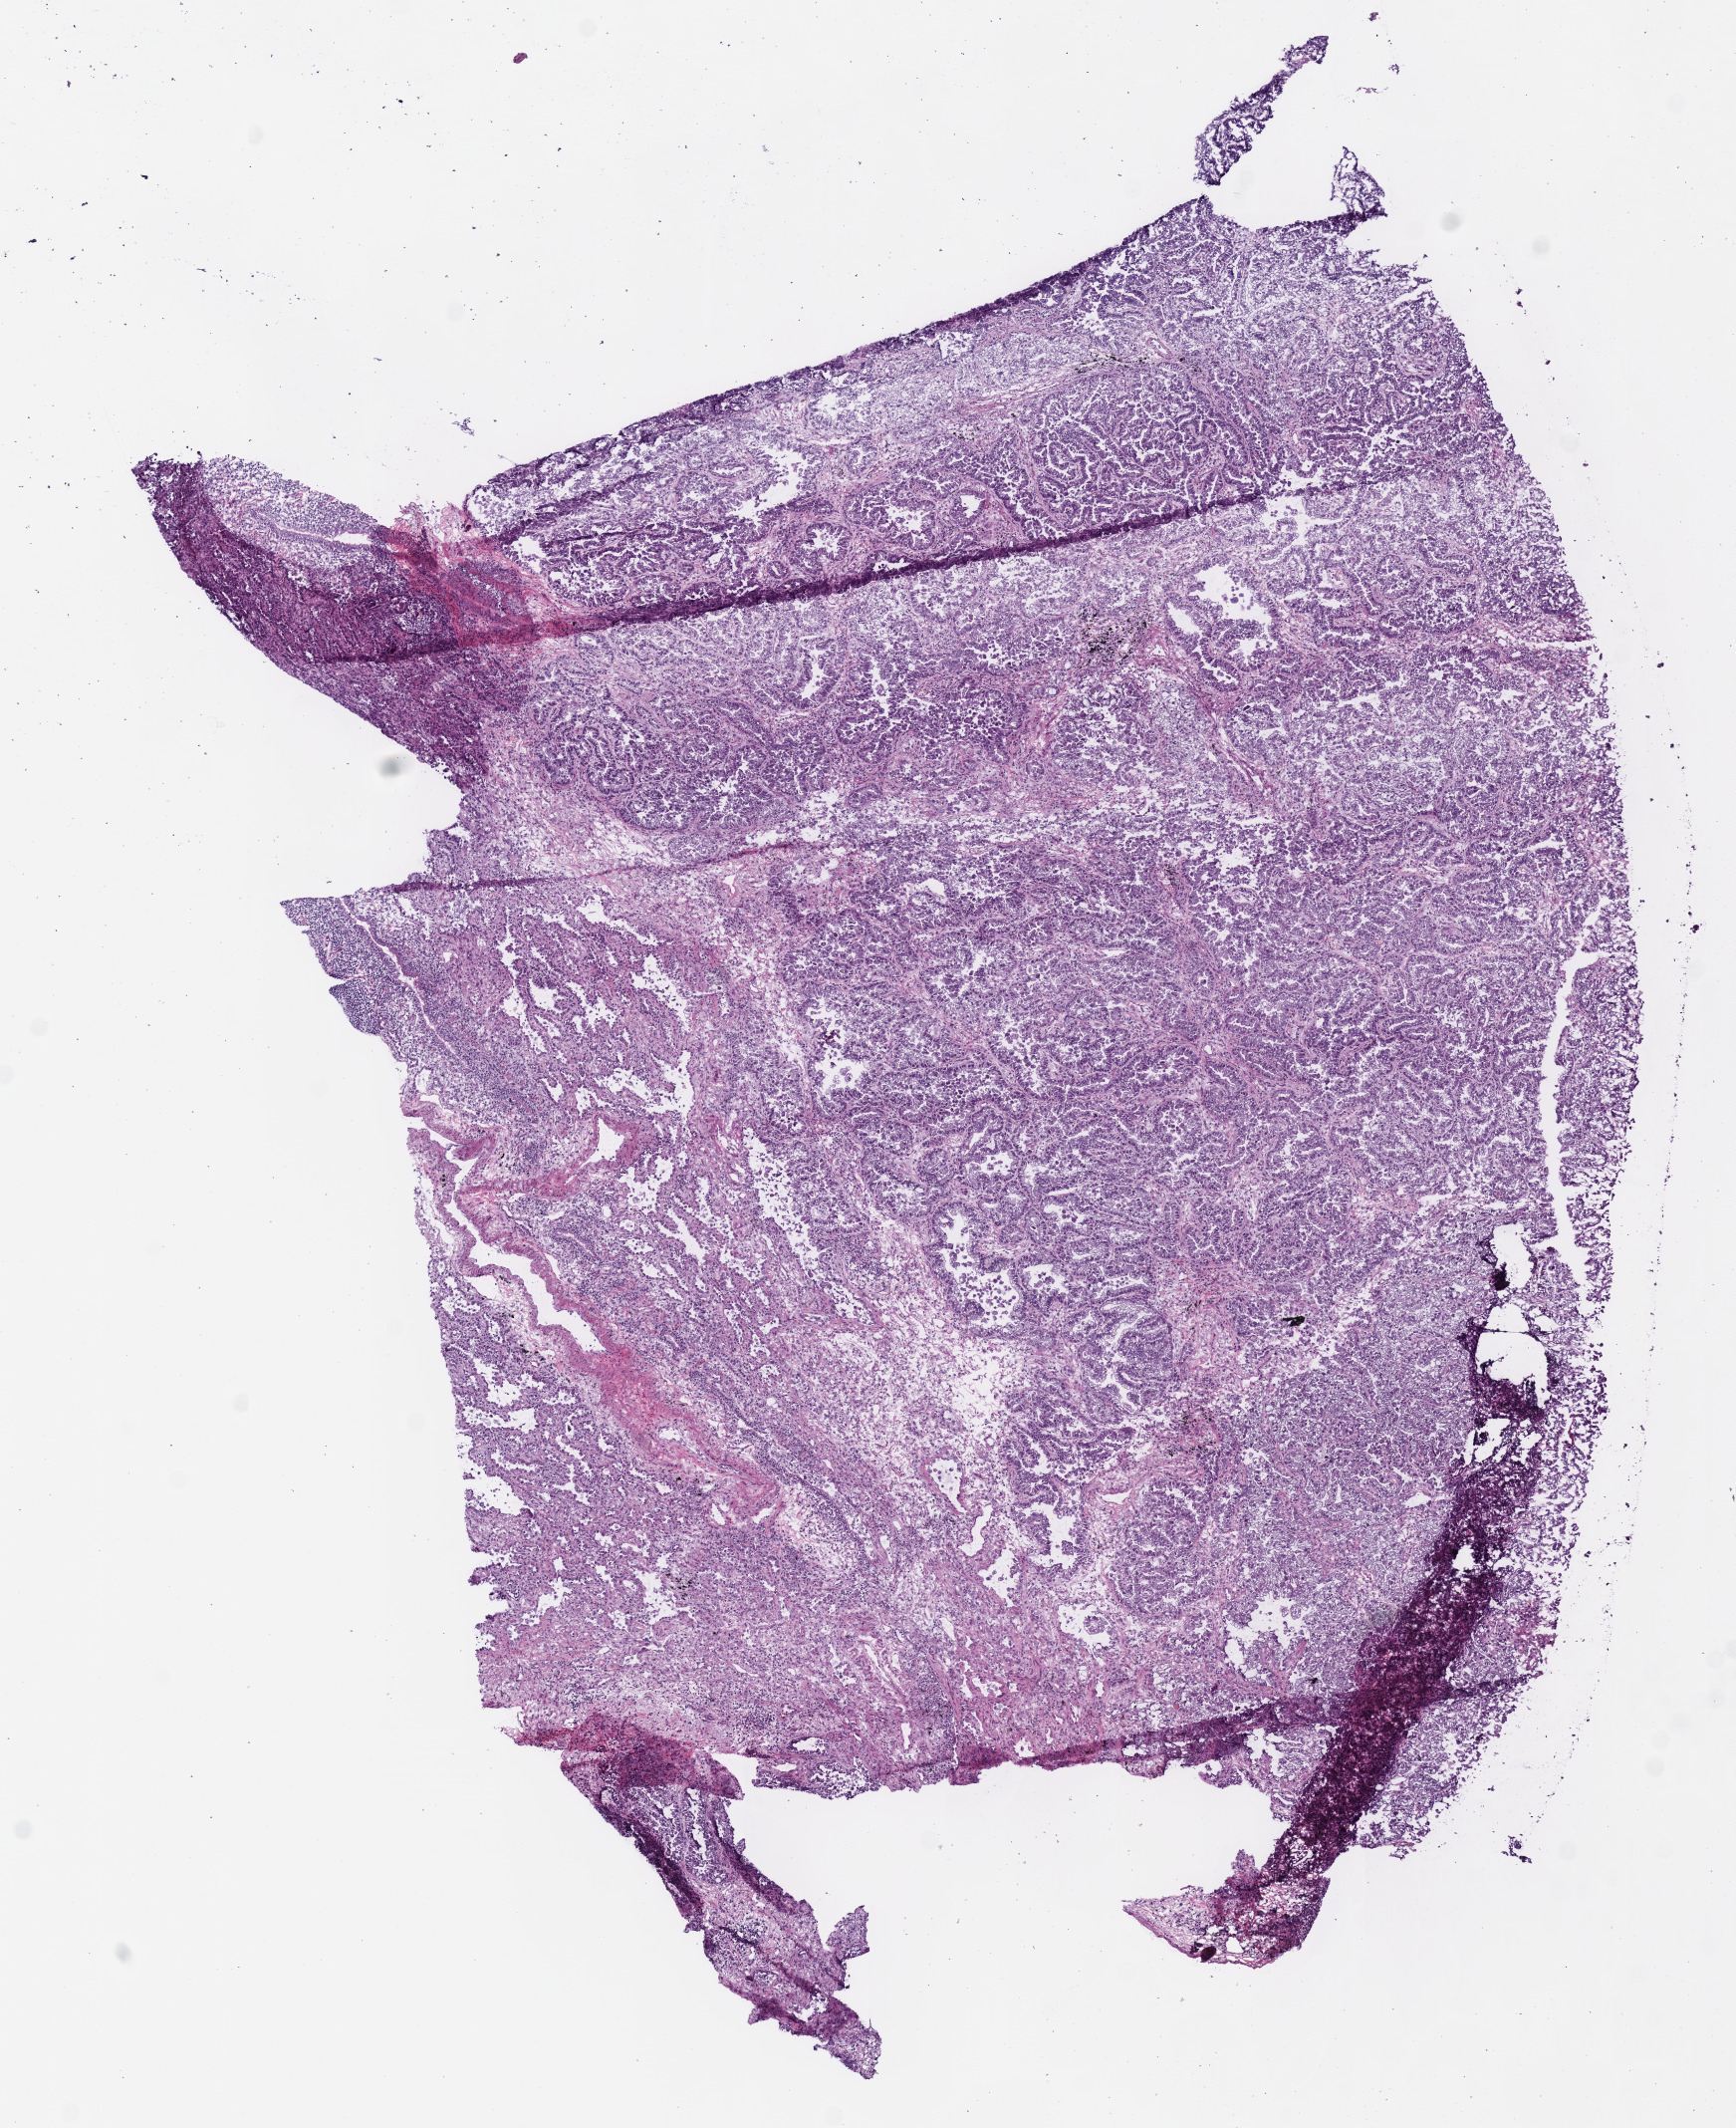
H&E-stained whole-slide image — whole scanned area (about 6.9 x 8.4 mm) shown as a low-resolution overview; frozen section; sample: primary tumour, lung. Female, age 80 years at initial diagnosis. Slide review estimates, as recorded: tumour cells 96%, tumour nuclei 80%, normal cells 0%, stromal cells 3%, necrosis 1%. Infiltration values recorded for this section: lymphocyte infiltration 2%, monocyte infiltration 3%.
TNM: T3 N0 M0. Diagnosis: Adenocarcinoma with mixed subtypes (upper lobe, lung). AJCC pathologic stage: IIB (6th edition).